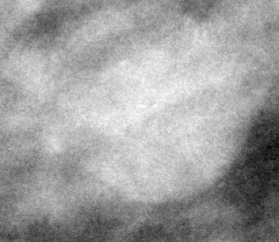
Cropped region of a digitized screen-film mammogram centred on a radiologist-marked abnormality; right breast; MLO view.
Marked abnormality: mass, shape round, margins circumscribed; BI-RADS assessment category 3; pathology result (as recorded, not read from the image): benign.